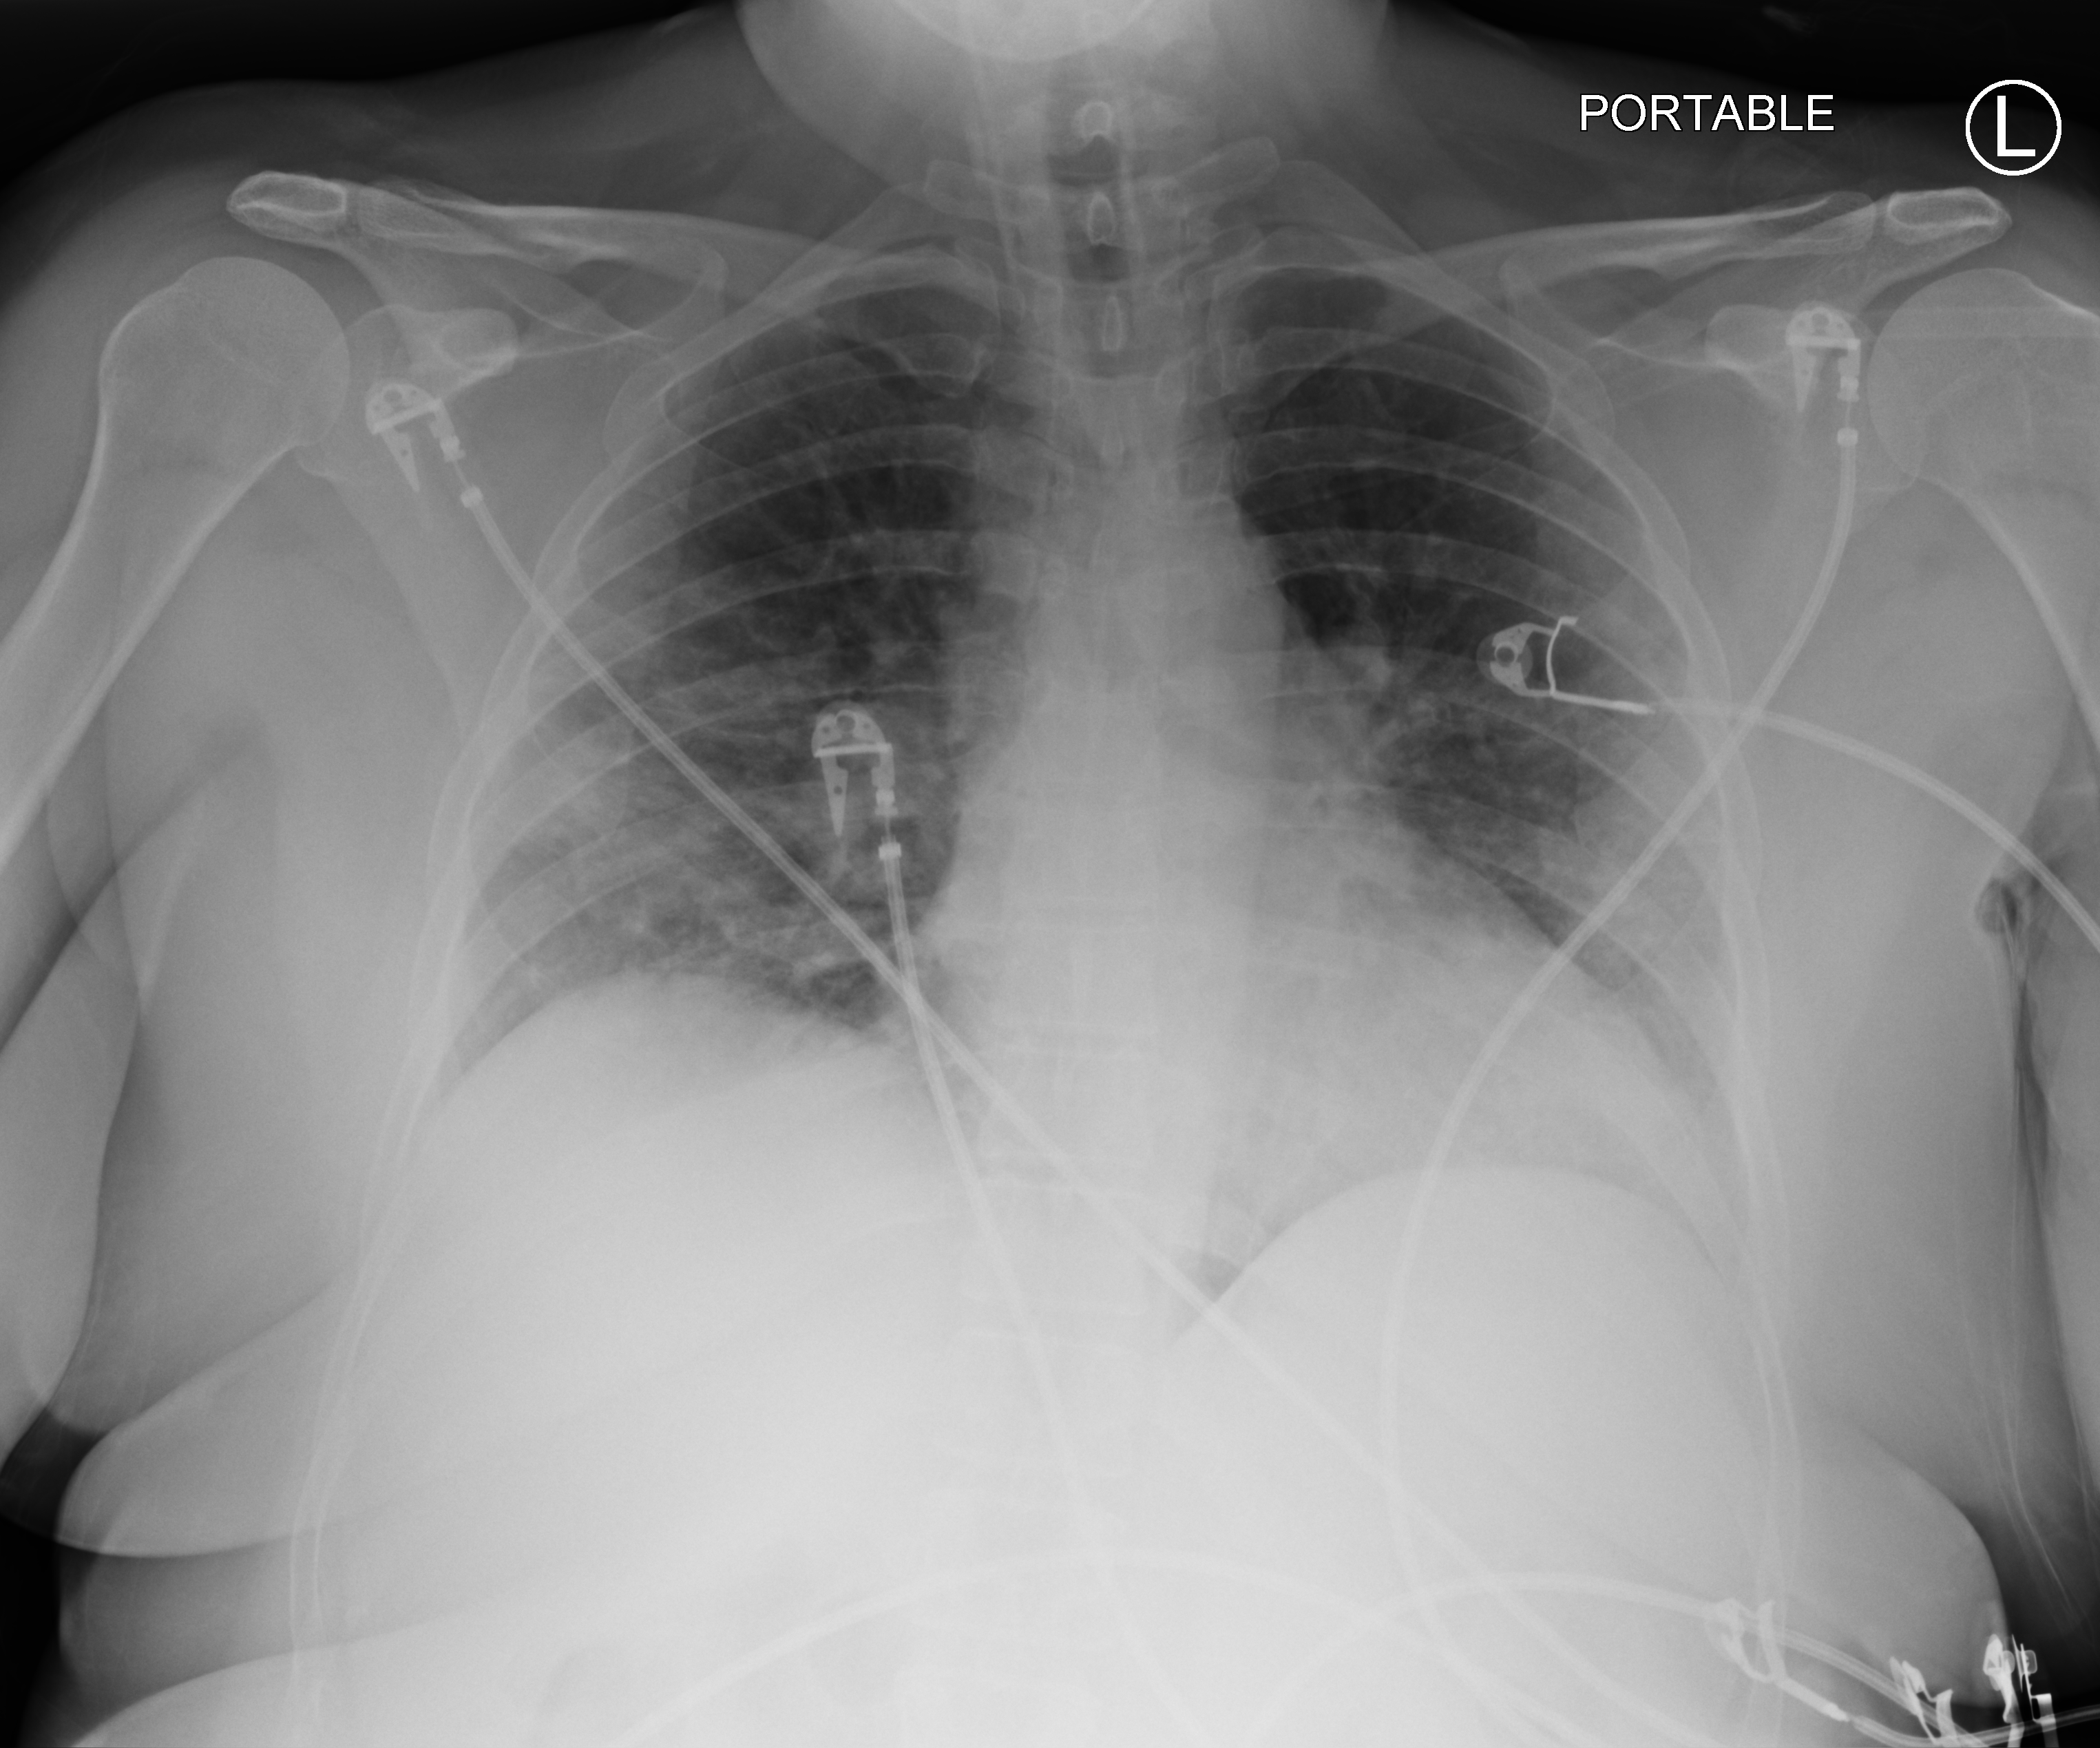
Bedside chest radiograph (computed radiography). Female patient hospitalised with COVID-19, age 18–59 years.
Admission-level facts for this patient (not findings on this image; timing relative to this image not recorded): admitted to intensive care during this hospital stay: yes; length of hospital stay: 31 days; hypertension (admission record): yes.